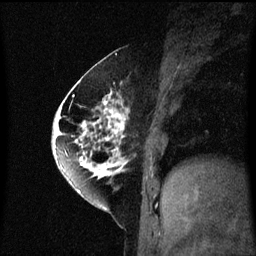
Breast MRI (dynamic contrast-enhanced), one sagittal slice. Slice 25 of 60 in the series (ordered by position). Dynamic contrast-enhanced series, image 2 of 3 at this slice position (ordered by acquisition). 1.5 T. TE 4.2 ms, TR 8.4 ms. 2 mm slice thickness. 256 × 256 image matrix, field of view 200 × 200 mm. Patient: female, 60 years.
Outlined on this slice (semi-automatic segmentation, software-assisted and operator-edited):
- analysis volume of interest (the breast-tissue region the enhancement analysis was run in; not a lesion): bounding box [x1, y1, x2, y2] px = [64, 70, 131, 195]
- tumour enhancement mask (voxels above the 70 % enhancement threshold inside the analysis volume of interest): [64, 82, 129, 193]